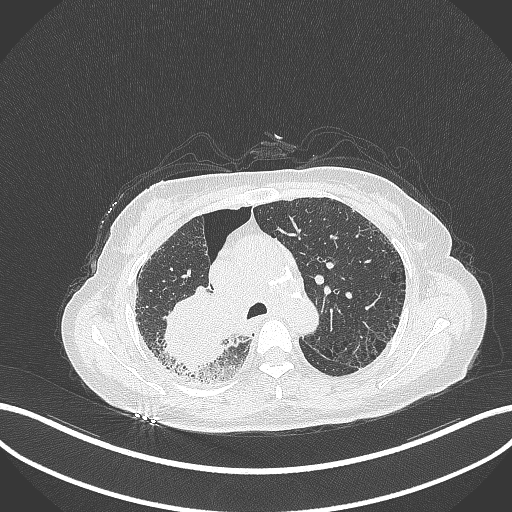
Chest CT, one axial slice; position 236 of 408 along the scan axis; 120 kVp; lung window (W 1500 / L -600 HU); 1 mm slice thickness; 512 × 512 image matrix, field of view 400 × 400 mm. Patient: female, 64 years. From the clinical record (not read from this slice): clinical TNM (as recorded): T3 N3 M0.
Structures marked on this image (bounding box drawn by a radiologist):
- lung tumour (recorded histology: squamous cell carcinoma): box from (x=162, y=283) to (x=239, y=375) px